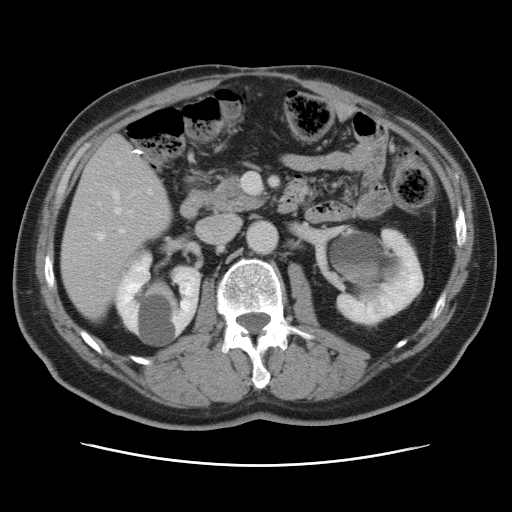
Contrast-enhanced abdominal CT, one axial slice. Position 32 of 80 along the scan axis. 120 kVp. Intravenous contrast given. Soft-tissue window (W 400 / L 40 HU). 5 mm slice thickness. 512 × 512 image matrix. Male patient, age 69 years. Case-level facts recorded for this patient, not image findings: diagnosis: colorectal cancer liver metastases, imaged before liver resection; multiple liver metastases: no; largest metastasis: 5 cm; chemotherapy before resection: no.
Outlined on this slice (expert manual segmentation):
- hepatic veins: box from (x=96, y=192) to (x=120, y=240) px
- liver: (x=62, y=136)–(x=171, y=318)
- planned liver remnant (the part of the liver to remain after resection): (x=62, y=212)–(x=158, y=318)
- portal vein (with intrahepatic branches): (x=101, y=228)–(x=125, y=277)